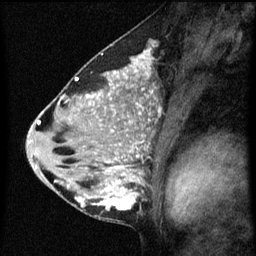
Breast MRI (dynamic contrast-enhanced), one sagittal slice; slice 32 of 60 in the series (ordered by position); dynamic contrast-enhanced series, image 2 of 3 at this slice position (ordered by acquisition); 1.5 T; TE 4.2 ms, TR 8 ms; 2.3 mm slice thickness; 256 × 256 image matrix, field of view 180 × 180 mm. Patient: female, 33 years.
Structures marked on this image (semi-automatic segmentation, software-assisted and operator-edited):
- analysis volume of interest (the breast-tissue region the enhancement analysis was run in; not a lesion): box from (x=71, y=118) to (x=150, y=215) px
- tumour enhancement mask (voxels above the 70 % enhancement threshold inside the analysis volume of interest): (x=77, y=156)–(x=138, y=211)